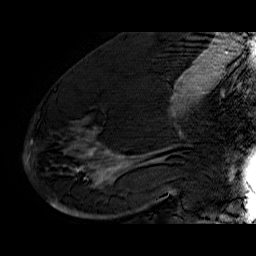
Breast MRI (dynamic contrast-enhanced), one sagittal slice. Slice 31 of 60 in the series (ordered by position). Dynamic contrast-enhanced series, time point 2 of 6 at this slice position (early post-contrast). 1.5 T. TE 6.4 ms, TR 32.9 ms. 4 mm slice thickness. 256 × 256 image matrix, field of view 200 × 200 mm. Female patient. From the clinical record (not read from this slice): setting: breast cancer imaged before/during neoadjuvant chemotherapy; receptor status: HR-positive, HER2-negative.
Annotated regions visible in this slice (semi-automatic segmentation, software-assisted and operator-edited):
- analysis volume of interest (the breast-tissue region the enhancement analysis was run in; not a lesion): bounding box (x1, y1, x2, y2) in pixels: (49, 74, 176, 210)
- tumour enhancement mask (voxels above the 100 % enhancement threshold inside the analysis volume of interest): (76, 113, 175, 195)